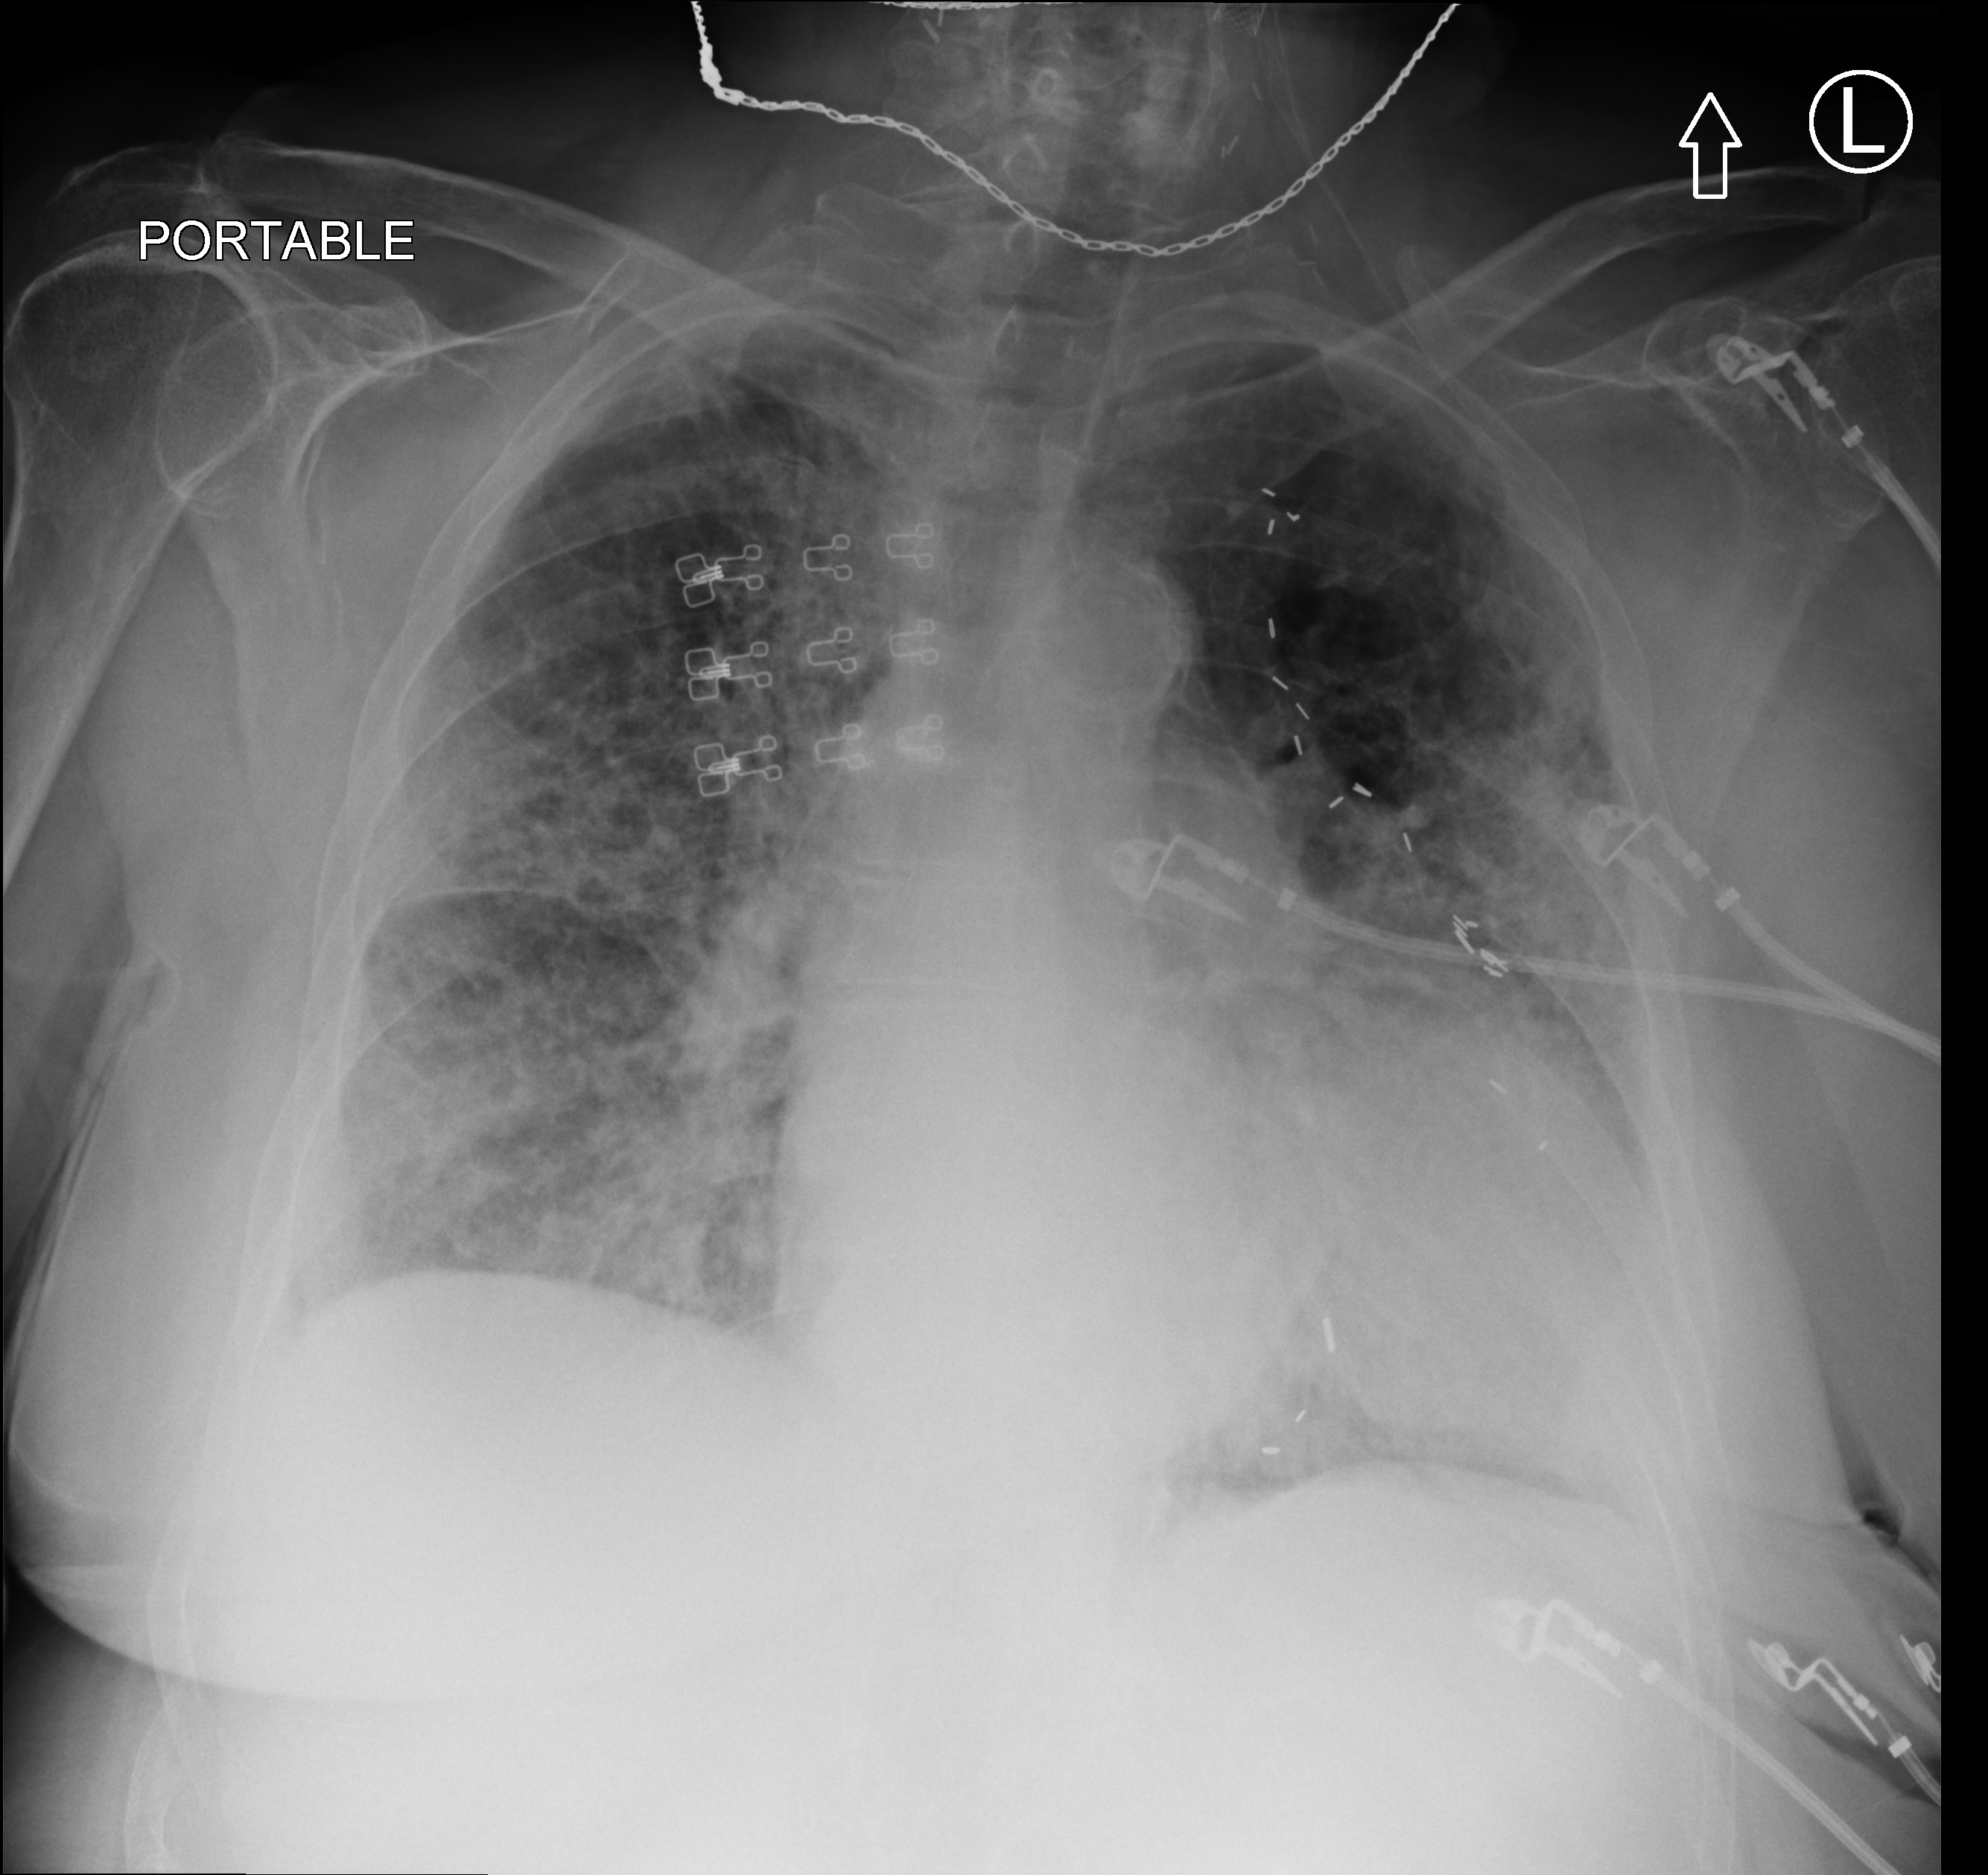
Bedside chest radiograph (computed radiography); anteroposterior (AP) projection. Patient hospitalised with COVID-19; female, aged 75–90 years.
From the hospital-stay record, not from the radiograph (when in the stay this image was taken is not recorded):
- mechanically ventilated during this hospital stay: no
- COPD (admission record): yes